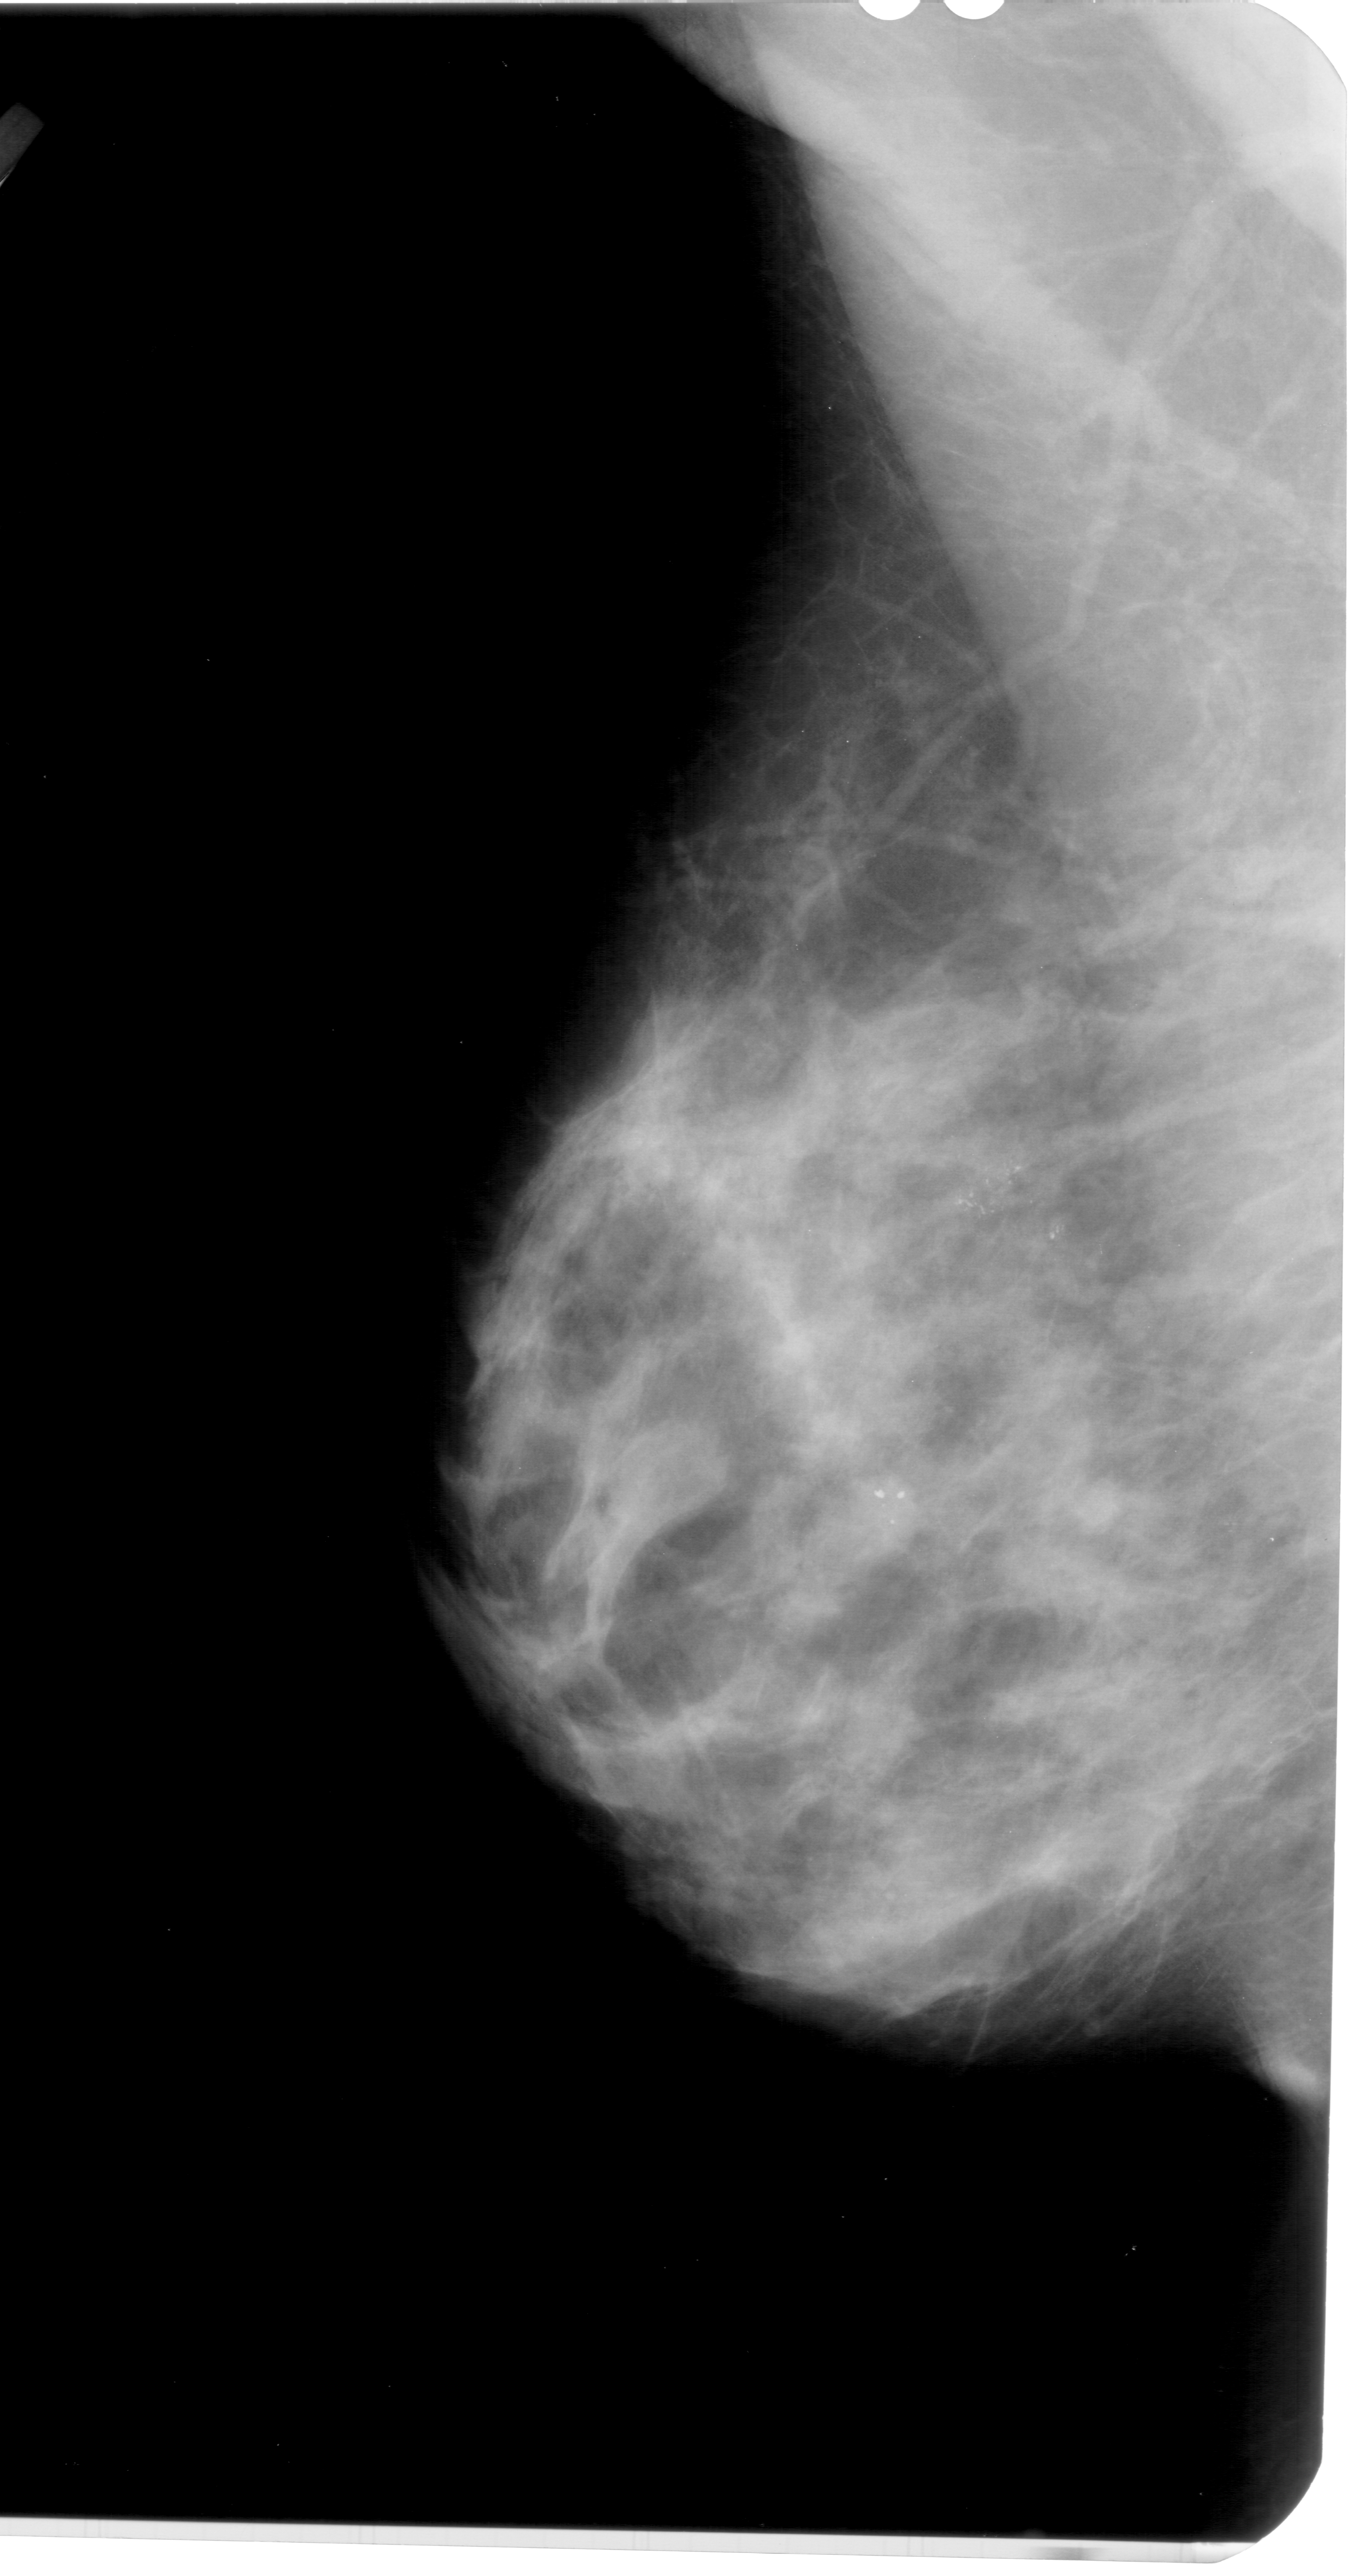
Scanned film-screen mammogram. Left breast. MLO view. Breast composition: extremely dense (BI-RADS density category 4 of 4). 1348 × 2576 image matrix.
Marked abnormalities (boxes around the expert regions of interest):
- calcifications, morphology pleomorphic, distribution clustered; BI-RADS assessment category 4; pathology result (as recorded, not read from the image): malignant: bounding box (x1, y1, x2, y2) in pixels: (936, 1145, 1088, 1264)